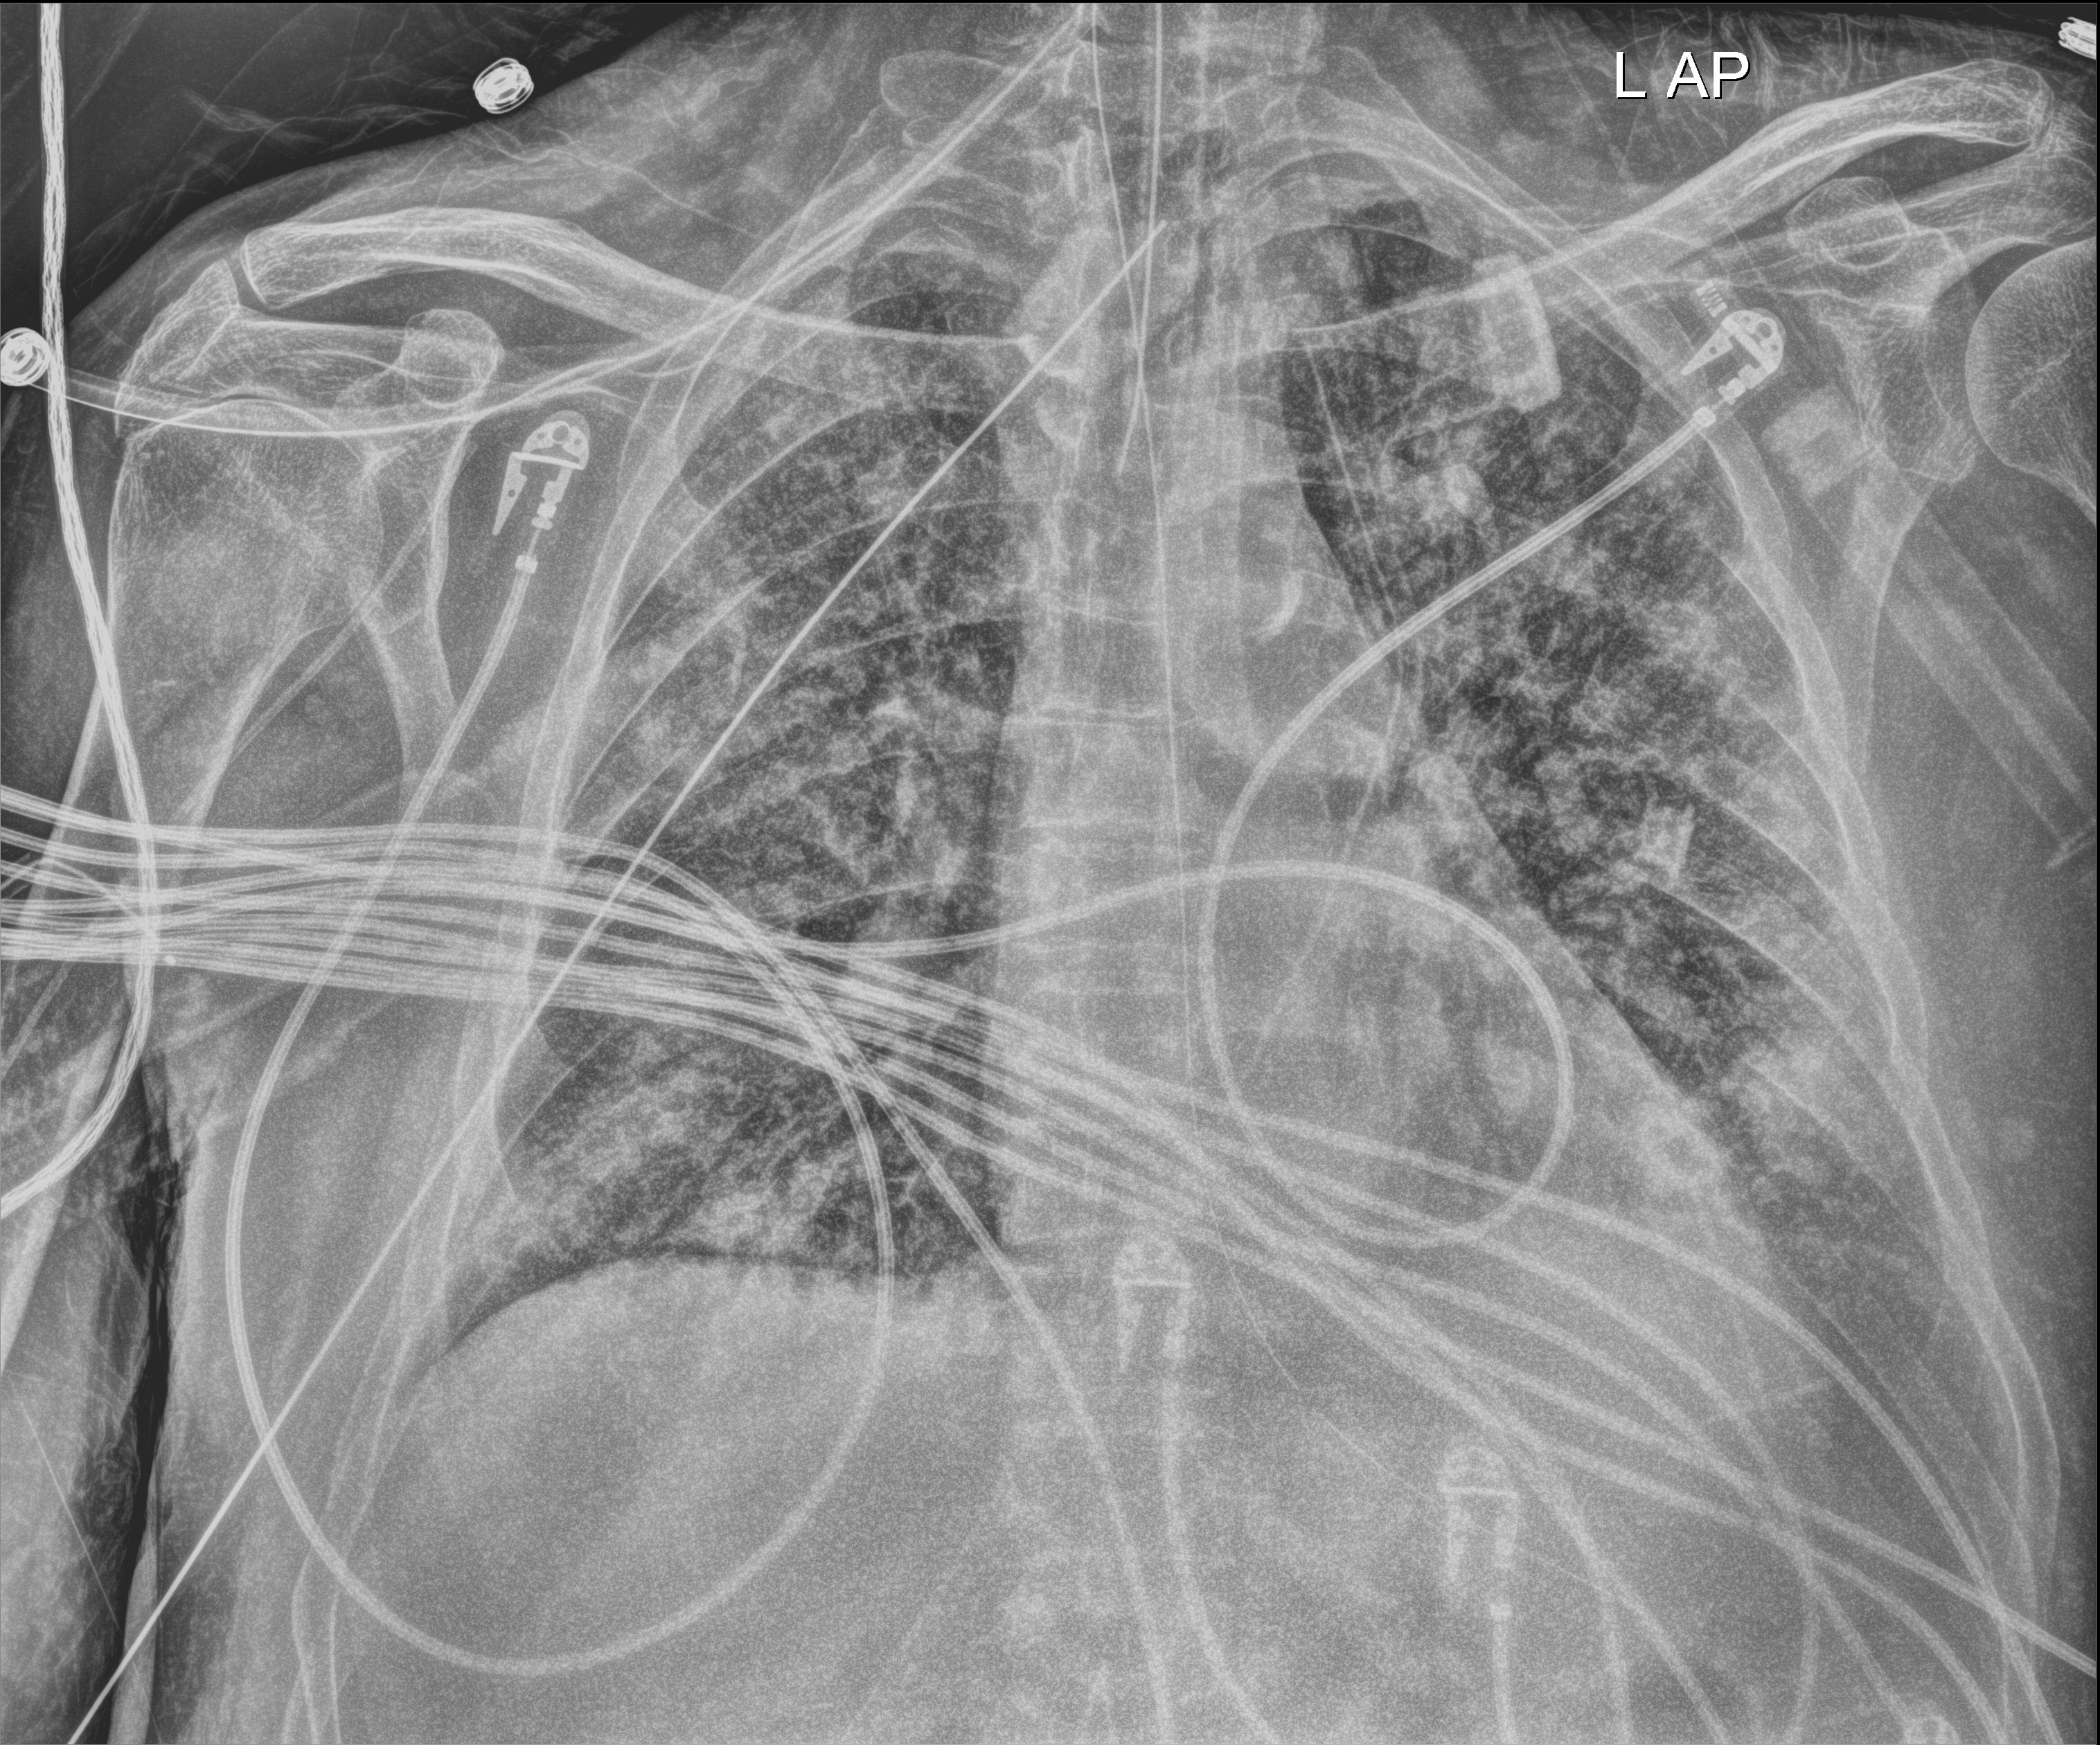
Bedside chest radiograph (digital radiography); anteroposterior (AP) projection. Male patient hospitalised with COVID-19, age 60–74 years.
From the hospital-stay record, not from the radiograph (when in the stay this image was taken is not recorded): hypertension (admission record): no; admitted to intensive care during this hospital stay: yes.